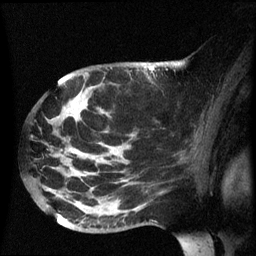
Breast MRI (dynamic contrast-enhanced), one sagittal slice. Position 40 of 60 along the scan axis. Dynamic contrast-enhanced series, image 2 of 3 at this slice position (ordered by acquisition). 1.5 T. TE 4.2 ms, TR 8.4 ms. 2.5 mm slice thickness. 256 × 256 image matrix, field of view 220 × 220 mm. Female patient, age 49 years.
Structures marked on this image (semi-automatic segmentation, software-assisted and operator-edited):
- analysis volume of interest (the breast-tissue region the enhancement analysis was run in; not a lesion): bounding box (x1, y1, x2, y2) in pixels: (29, 72, 185, 233)
- tumour enhancement mask (voxels above the 70 % enhancement threshold inside the analysis volume of interest): (76, 112, 79, 121)